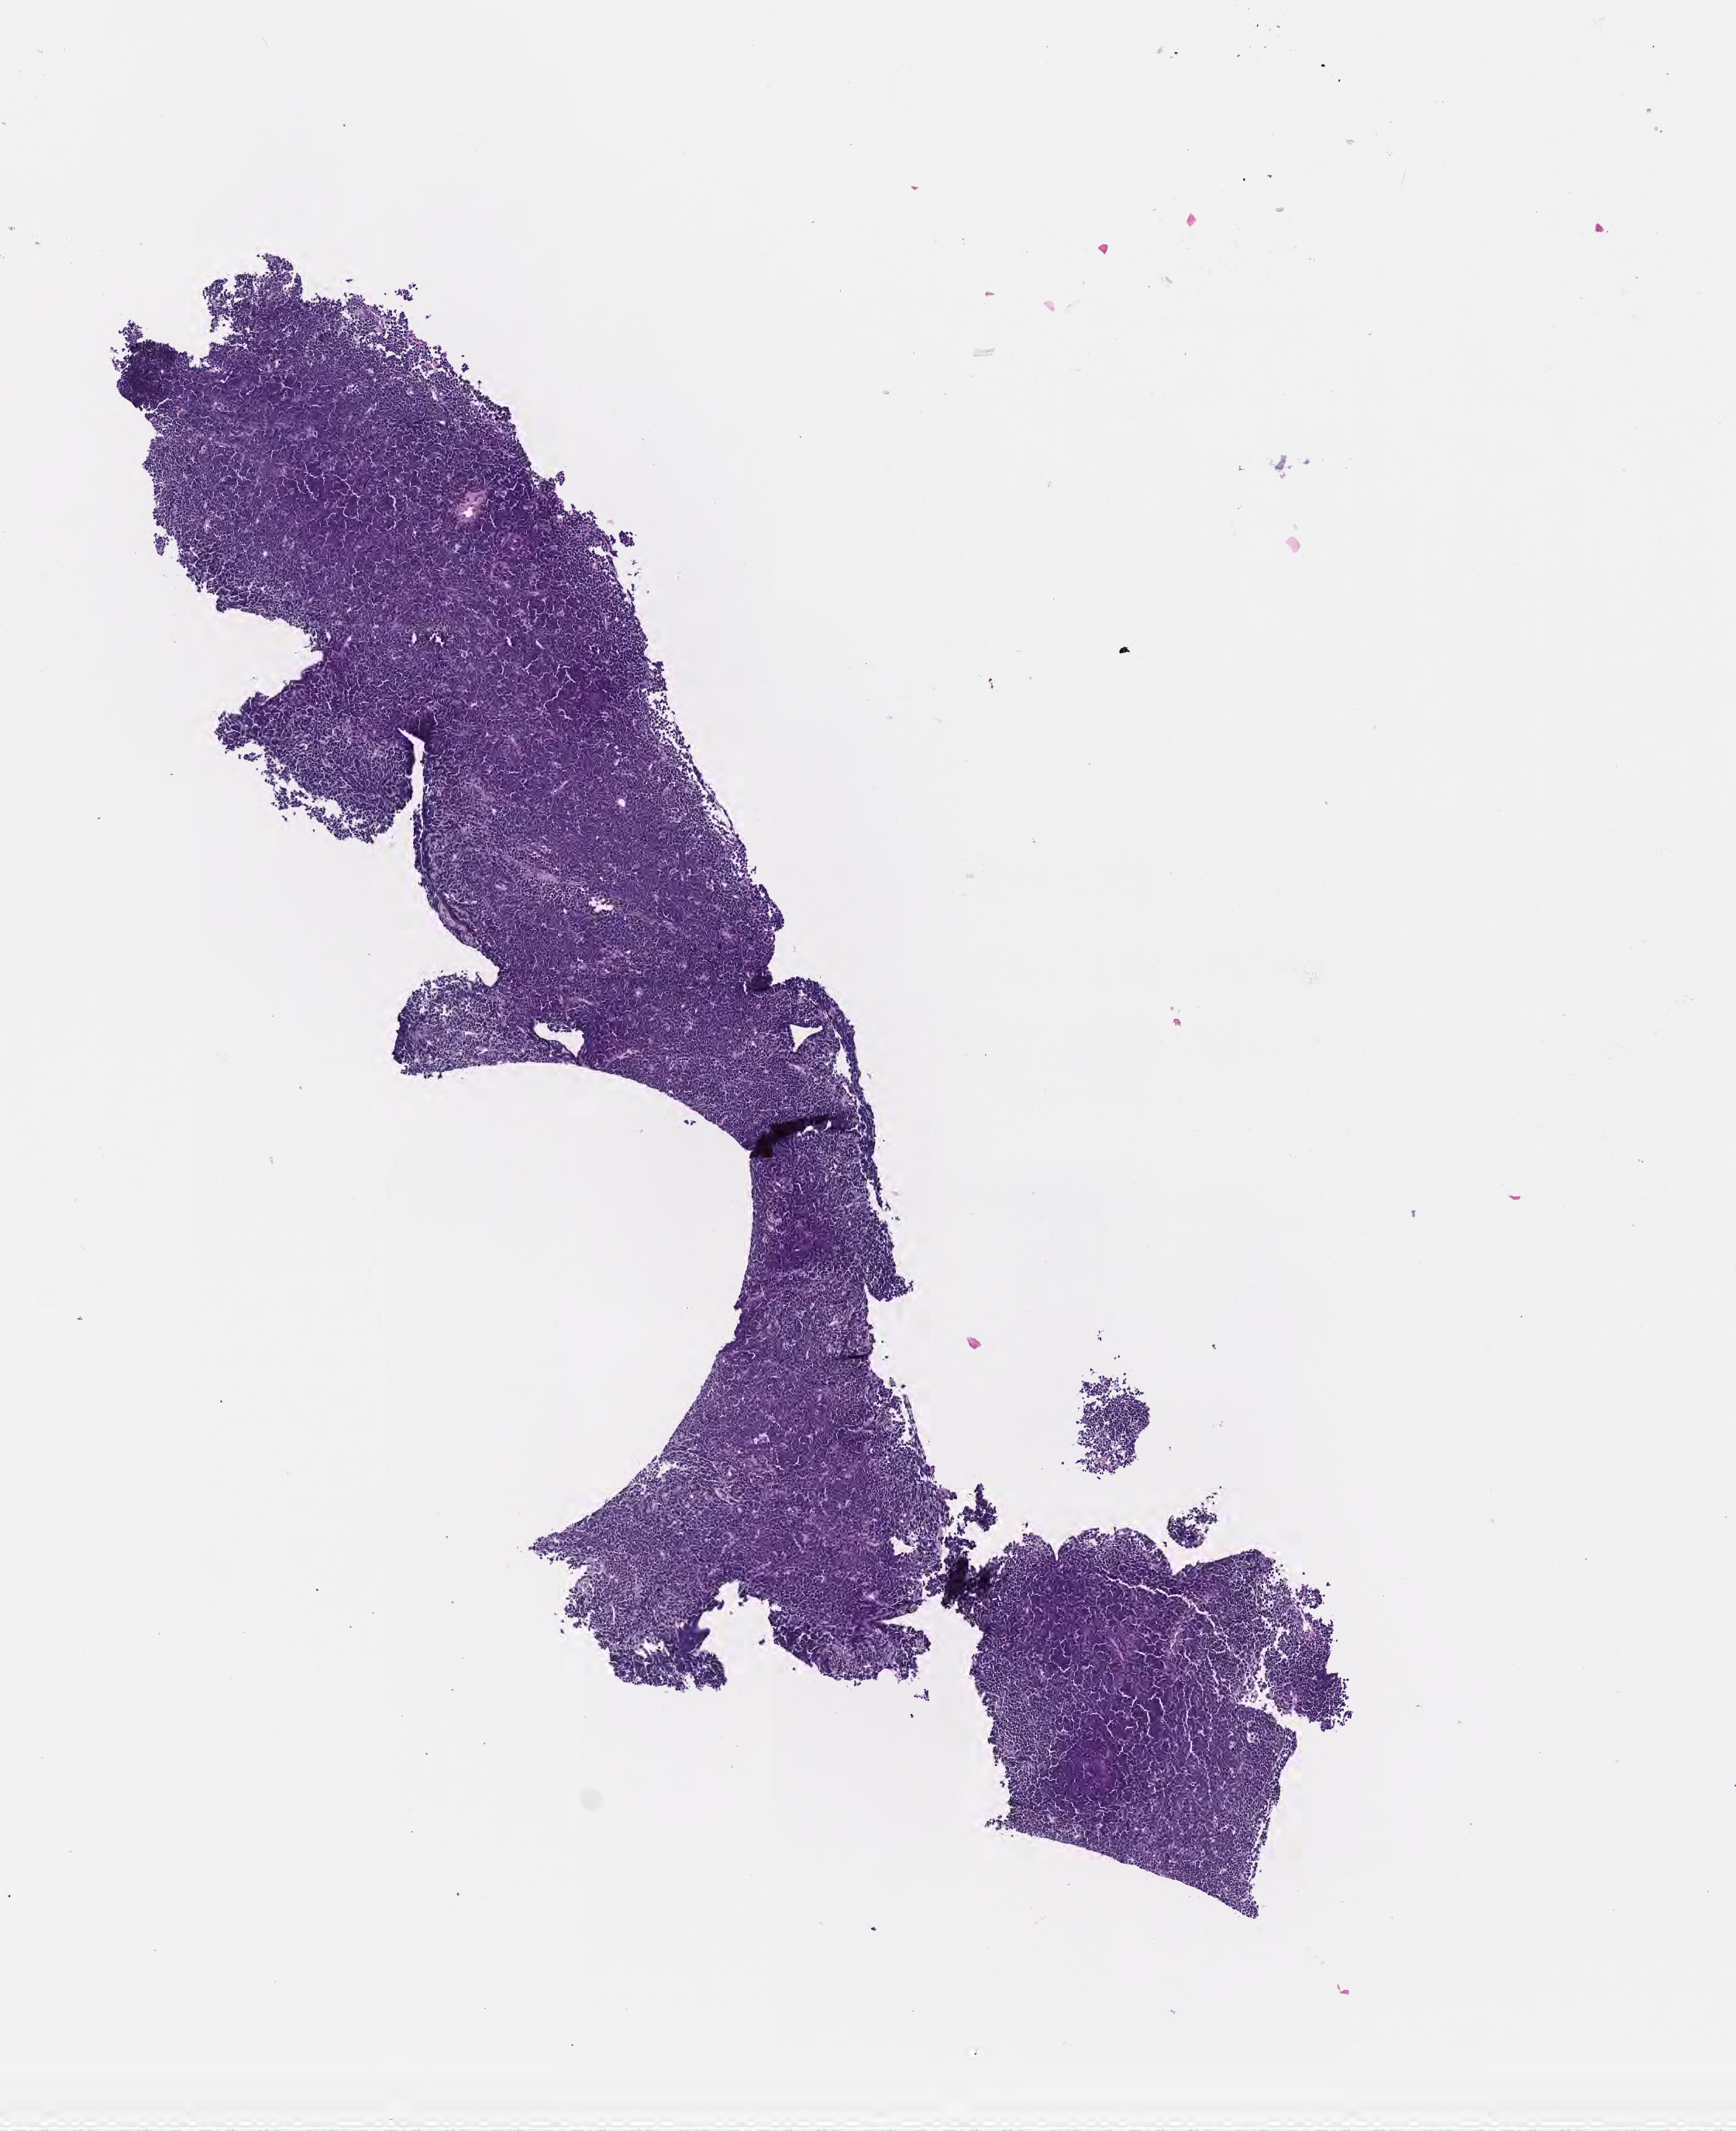
Digitized haematoxylin and eosin-stained section, whole scanned area (about 4.5 x 5.6 mm) shown as a low-resolution overview, tumor tissue. Male patient; age at initial diagnosis 5 years.
* diagnosis: Burkitt lymphoma, NOS